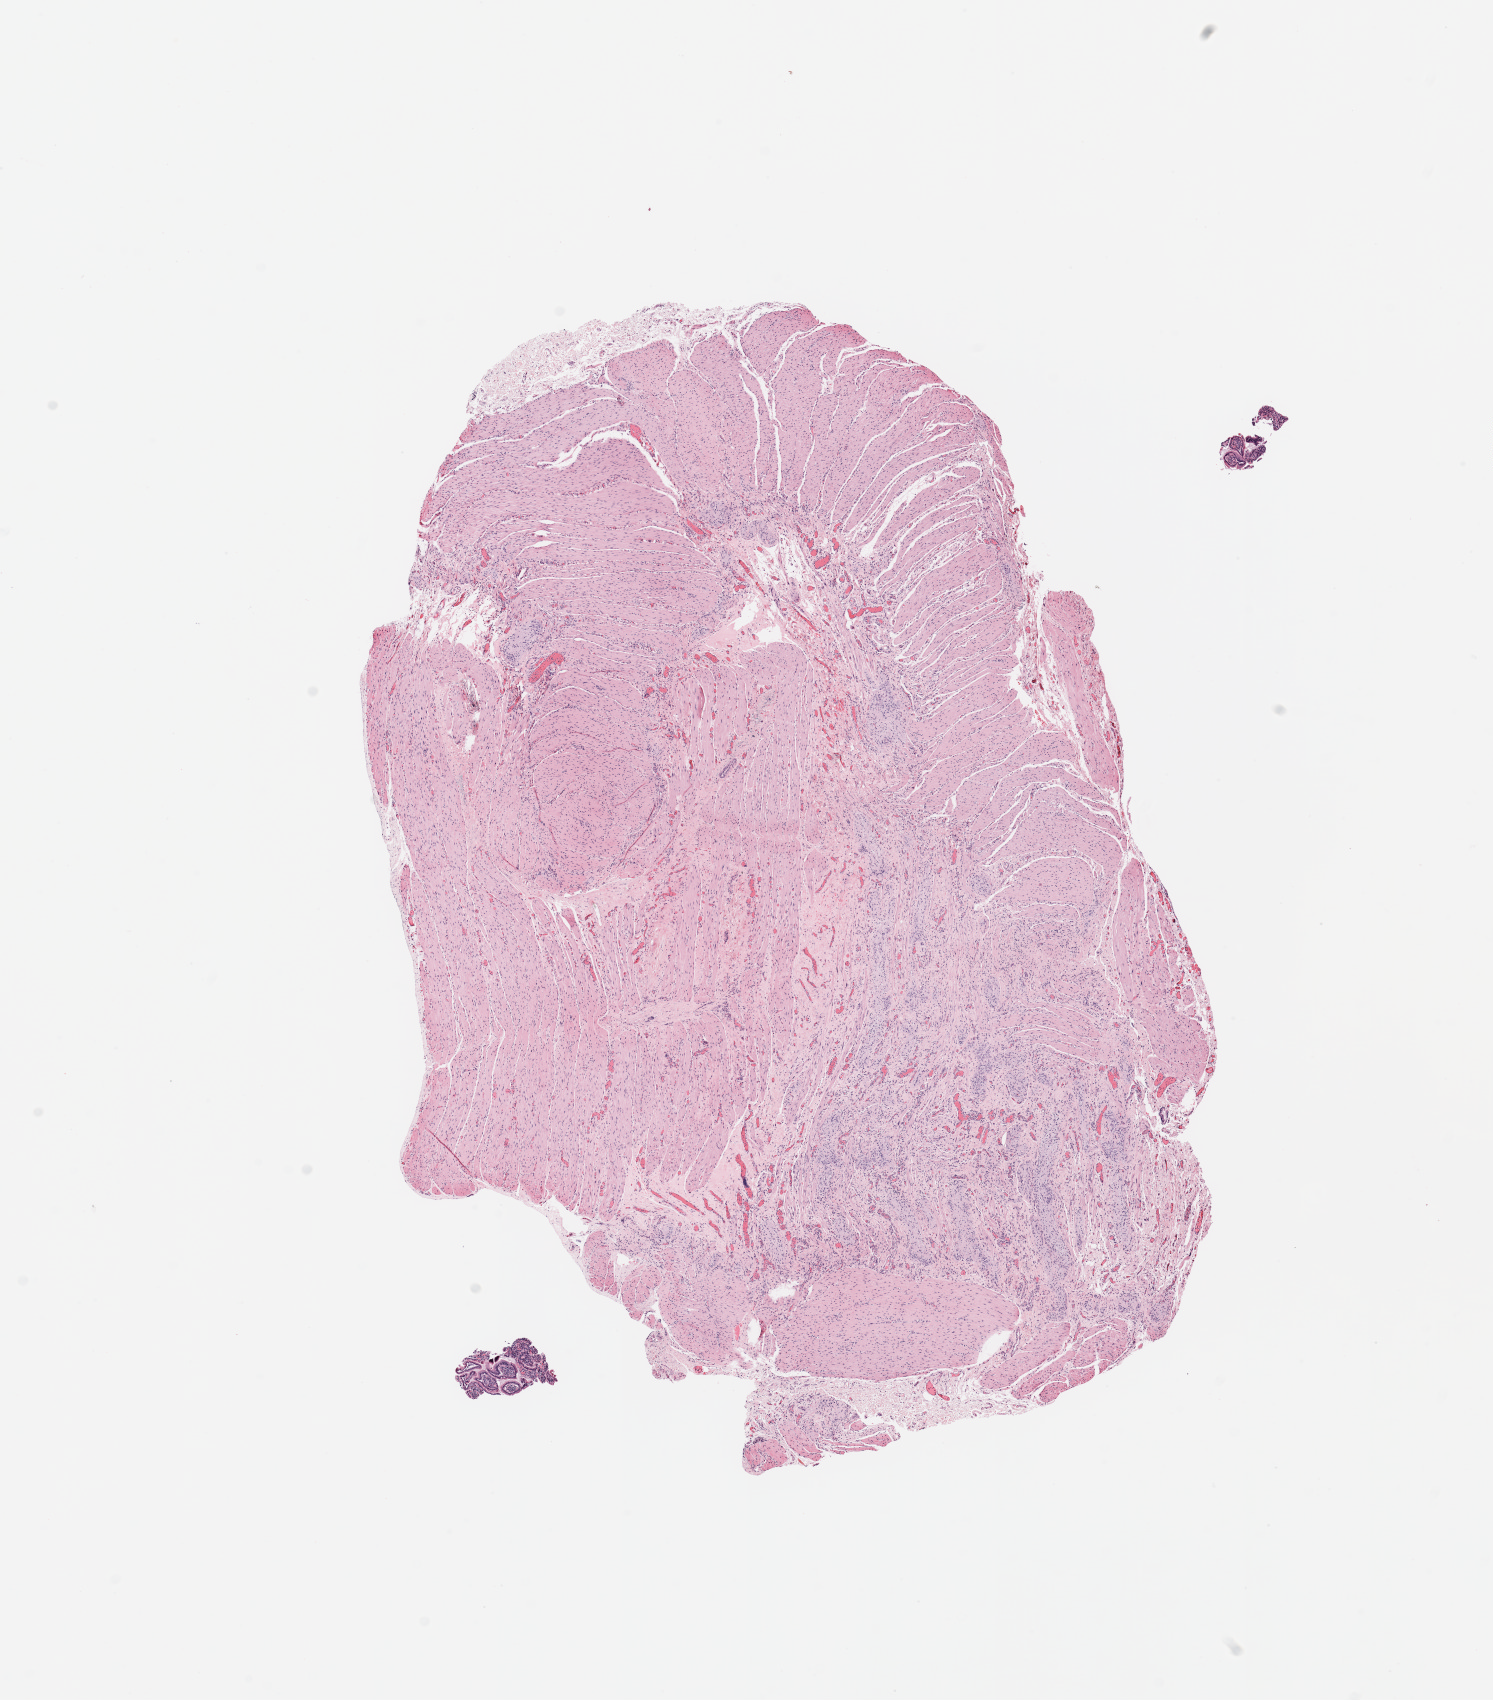
H&E whole-slide image, low-resolution overview of the scanned area, about 11.8 x 13.5 mm (acquisition: 20x scan), normal (non-tumour) tissue sample, sampled site: pancreas. 73-year-old female patient.
This section: normal (non-tumour) tissue from the same patient. Patient diagnosis: Infiltrating duct carcinoma, NOS.